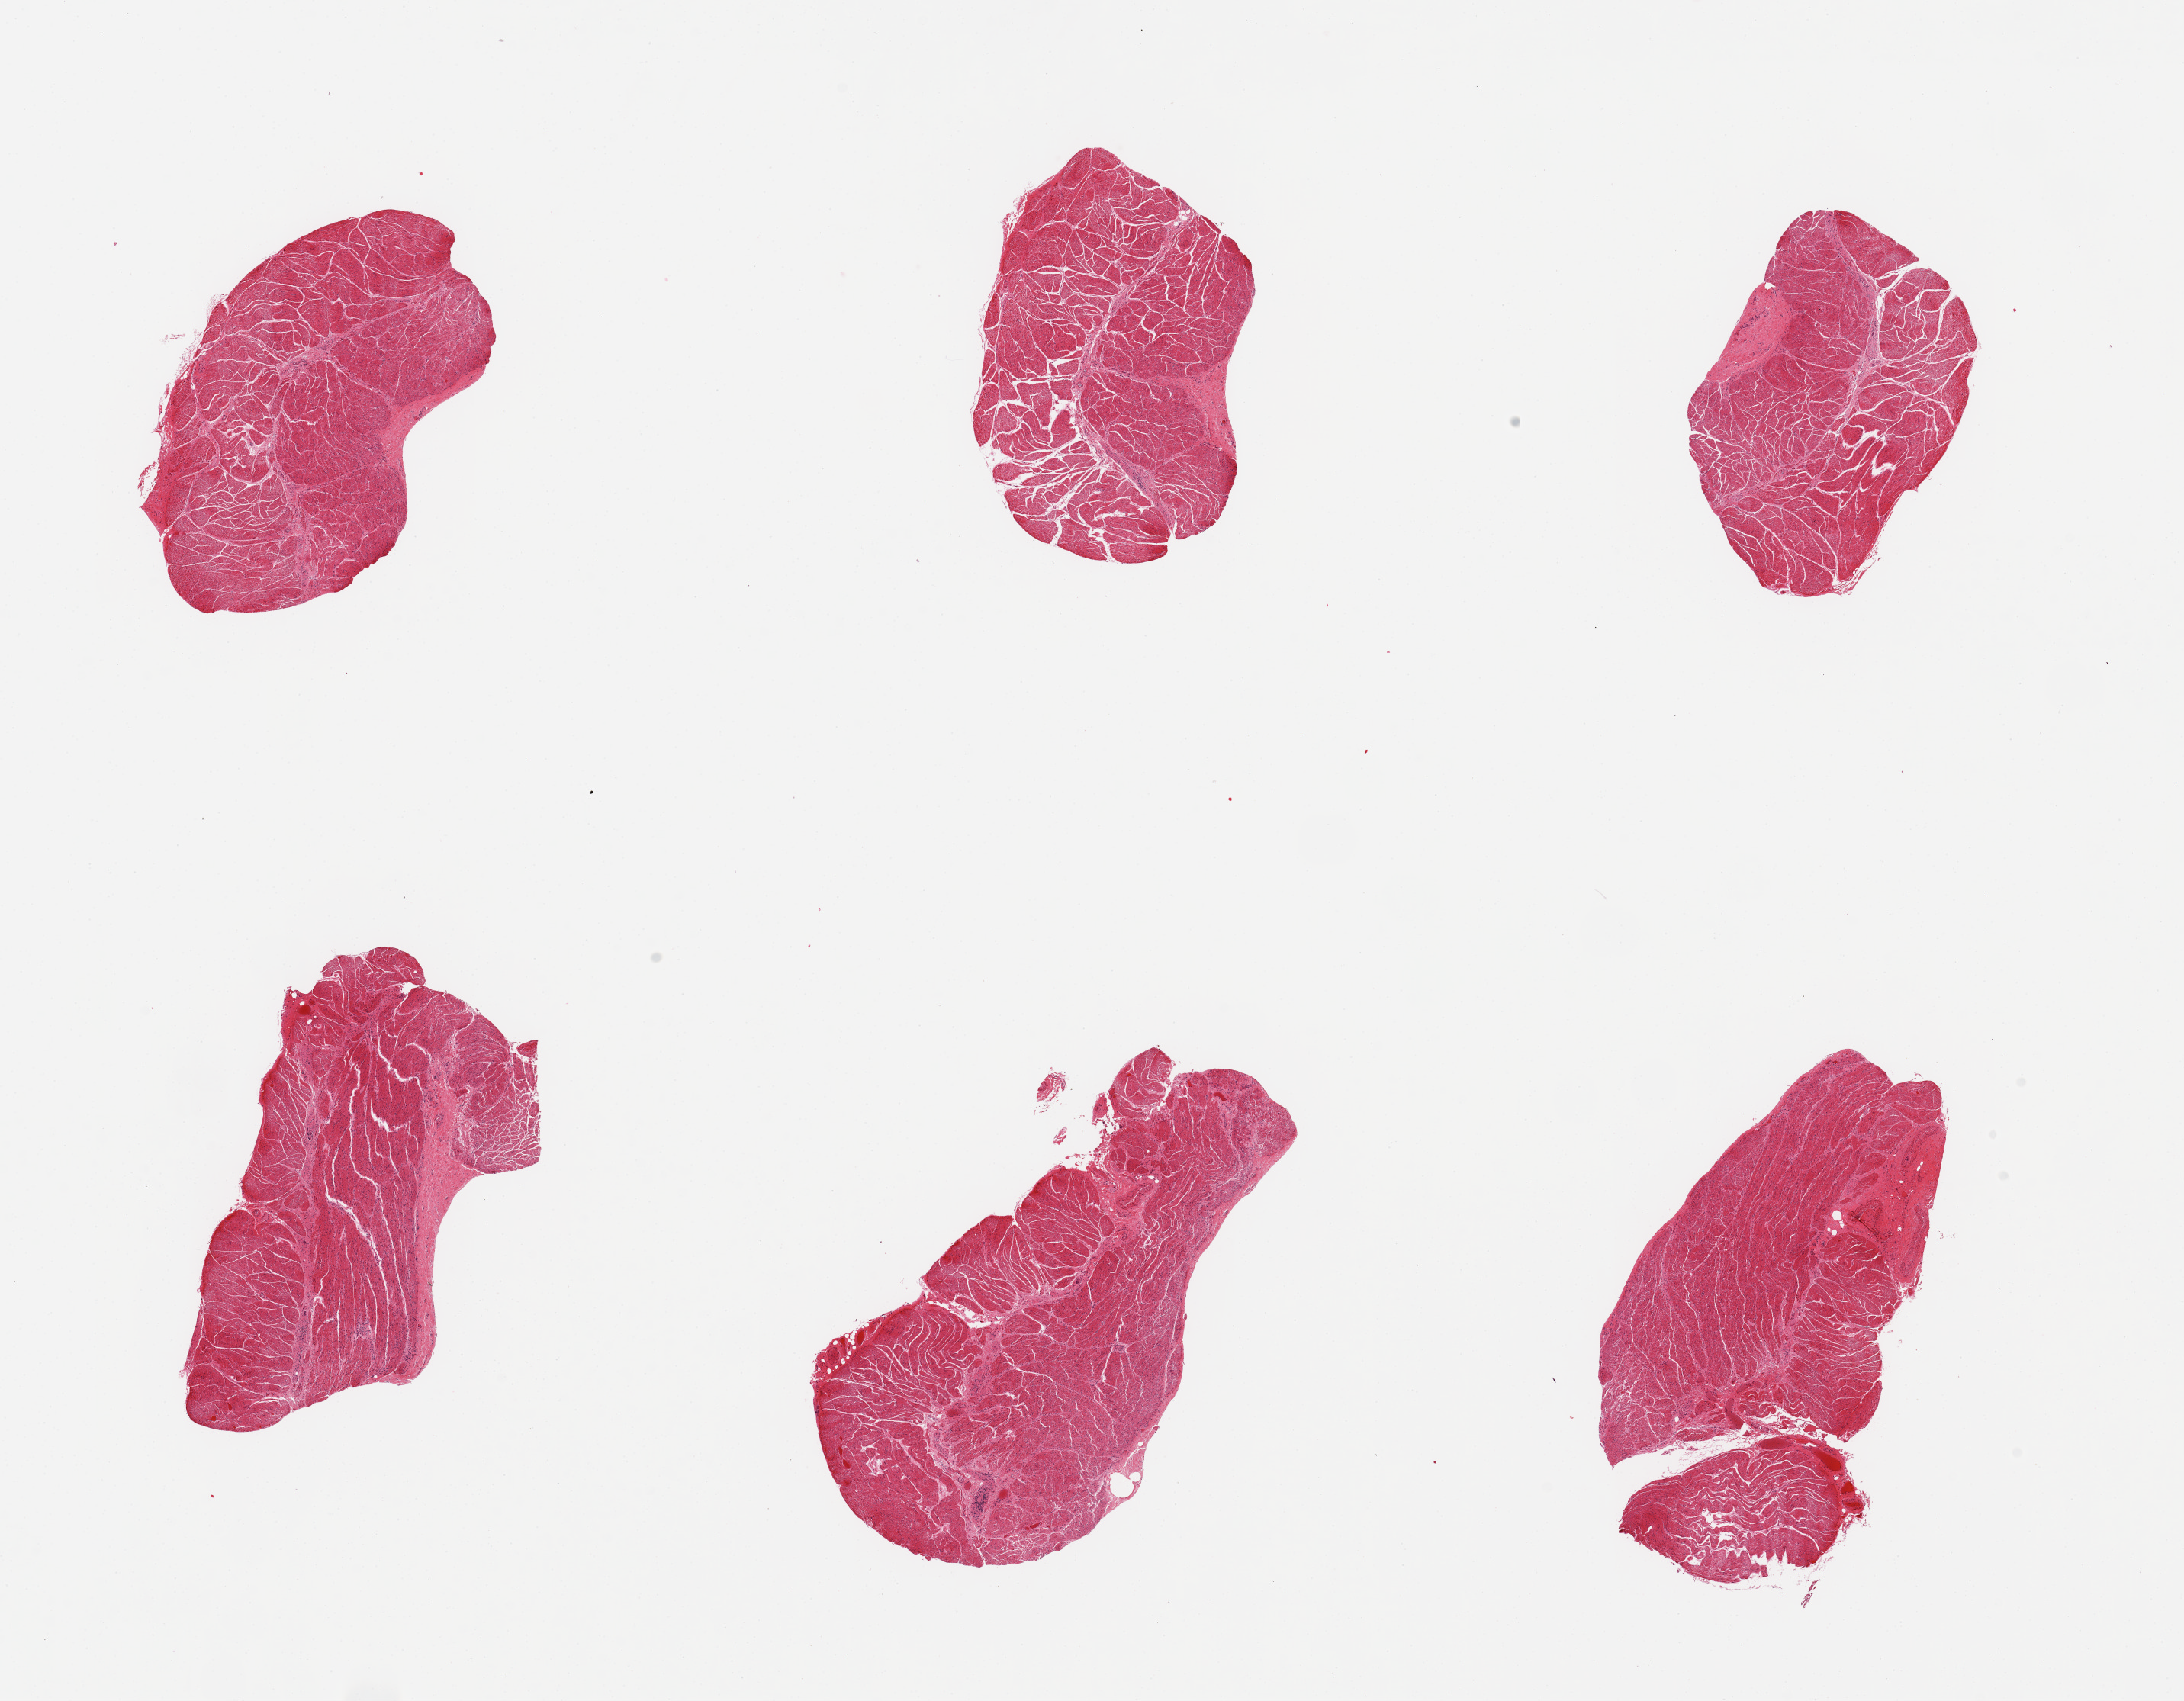
Hematoxylin and eosin (H&E) whole-slide image, brightfield — a low-resolution overview of the entire scanned area, about 22.6 x 17.6 mm (acquisition: 20x scan). PAXgene-fixed paraffin-embedded (PFPE) section. Sampled site (target tissue): esophageal muscle. Tissue donor sample. Donor: male.
Review note (as recorded): 6 pieces; well trimmed muscularis.